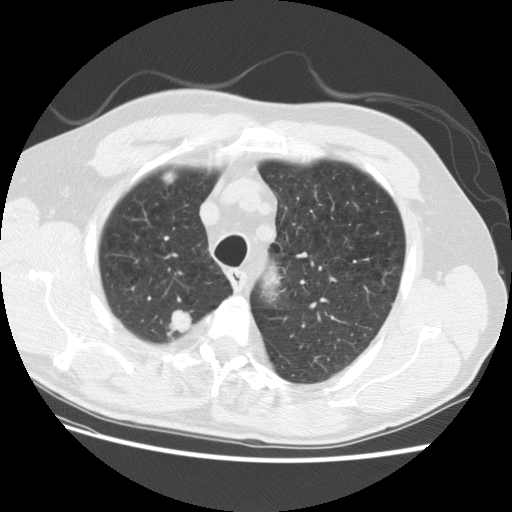
Low-dose screening chest CT, one axial slice. Position 100 of 124 along the scan axis. Reconstruction kernel STANDARD. 140 kVp. Lung window (W 1500 / L -600 HU). 2.5 mm slice thickness. 512 × 512 image matrix, field of view 361 × 361 mm.
Annotated regions visible in this slice (manually delineated by an expert):
- lesion 1 (tumor, upper lobe of right lung): box from (x=168, y=310) to (x=191, y=335) px